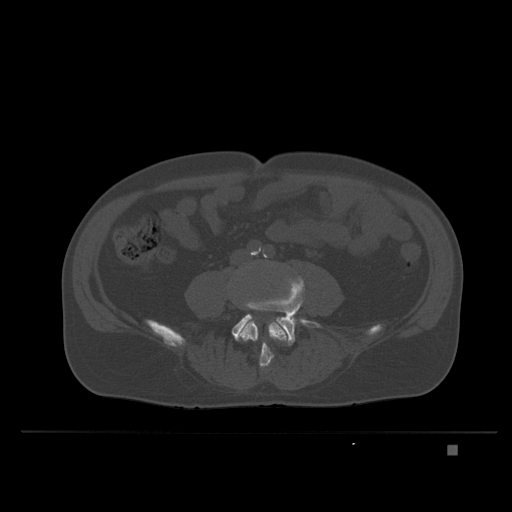
CT including the spine, one axial slice; slice 66 of 435 in the series (ordered by position); bone window (W 1800 / L 400 HU); 512 × 512 image matrix, field of view 434 × 434 mm. Male patient, age 73 years. From the clinical record (not read from this slice): primary cancer: skin.
Outlined on this slice (semi-automatically segmented with operator editing):
- L4 vertebra: bounding box <238,318,288,373> (left, top, right, bottom; pixels)
- L5 vertebra: <232,280,322,346>